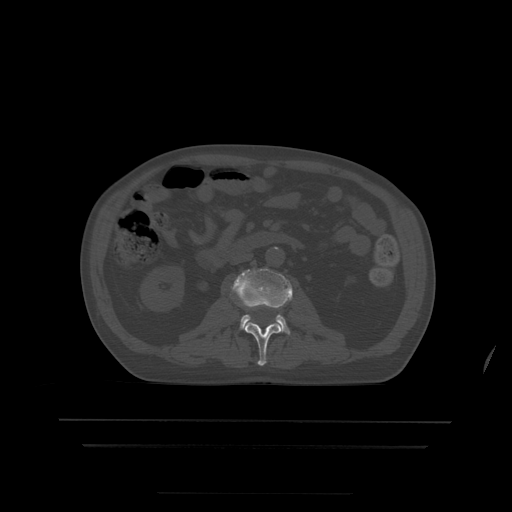
CT including the spine, one axial slice; slice 134 of 522 in the series (ordered by position); bone window (W 1800 / L 400 HU); 512 × 512 image matrix, field of view 436 × 436 mm. Patient age 68 years. From the clinical record (not read from this slice): primary cancer: urothelial.
Outlined on this slice (semi-automatic segmentation, software-assisted and operator-edited):
- L2 vertebra: bounding box <245,322,281,366> (left, top, right, bottom; pixels)
- L3 vertebra: <231,269,293,334>